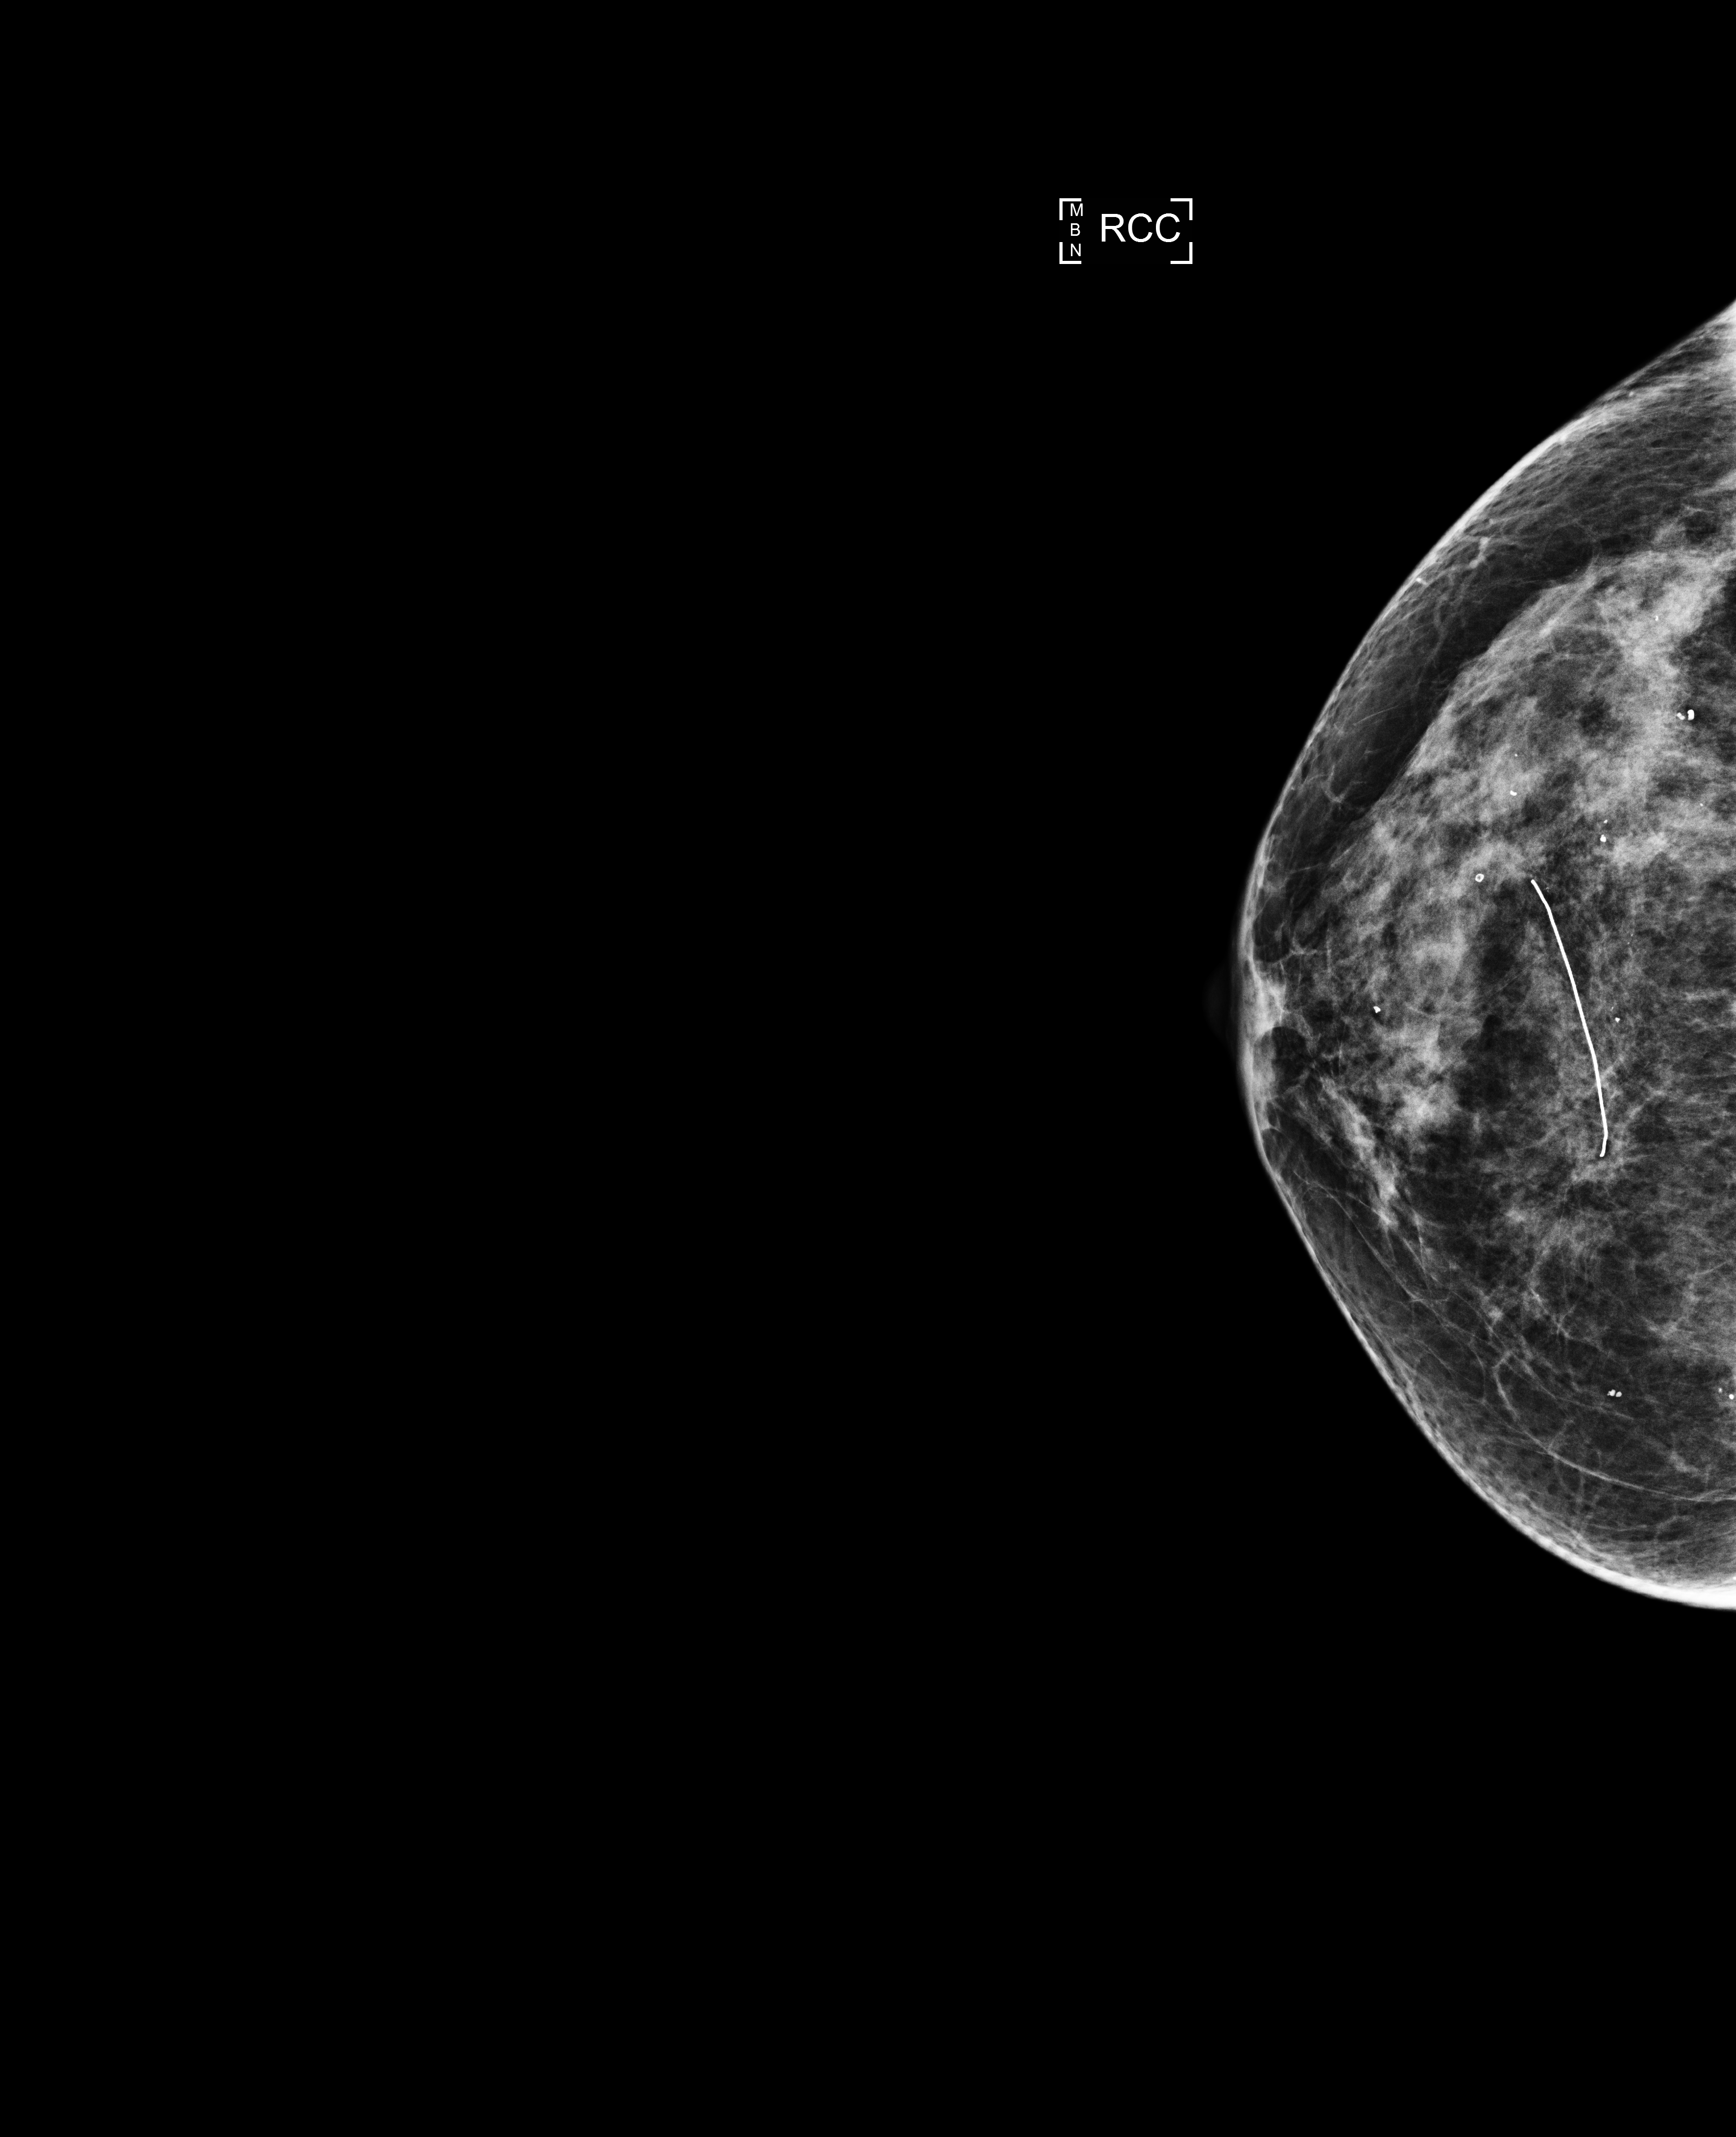
Screening examination, system: Selenia Dimensions. Patient: female, 75 years.
Image type: full-field digital mammogram. Breast: right. Projection: craniocaudal (CC) view.